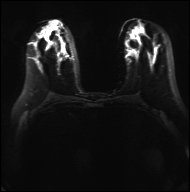
Breast MRI, one axial slice; diffusion-weighted series; image 2 of 4 stored at this slice position (different b-values; order by instance number); 3 T; 4 mm slice thickness; 190 × 192 image matrix, field of view 317 × 320 mm. Female patient.
Structures marked on this image (outlined manually by an expert reader):
- tumour on diffusion-weighted imaging: box from (x=44, y=47) to (x=63, y=56) px